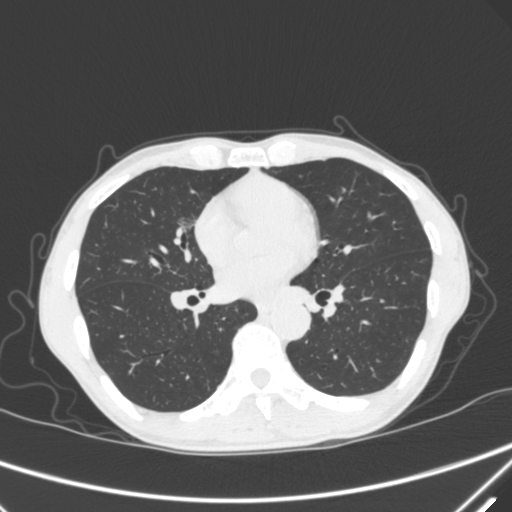
Chest CT, one axial slice; position 160 of 340 along the scan axis; 120 kVp; lung window (W 1500 / L -600 HU); 512 × 512 image matrix, field of view 350 × 350 mm. Patient: male, 67 years. From the clinical record (not read from this slice): clinical TNM (as recorded): T1c N0 M0; histopathological grade: G1-2.
Outlined on this slice (rectangle marked by the reading radiologist):
- lung tumour (recorded histology: adenocarcinoma): bounding box [x1, y1, x2, y2] px = [172, 209, 193, 245]